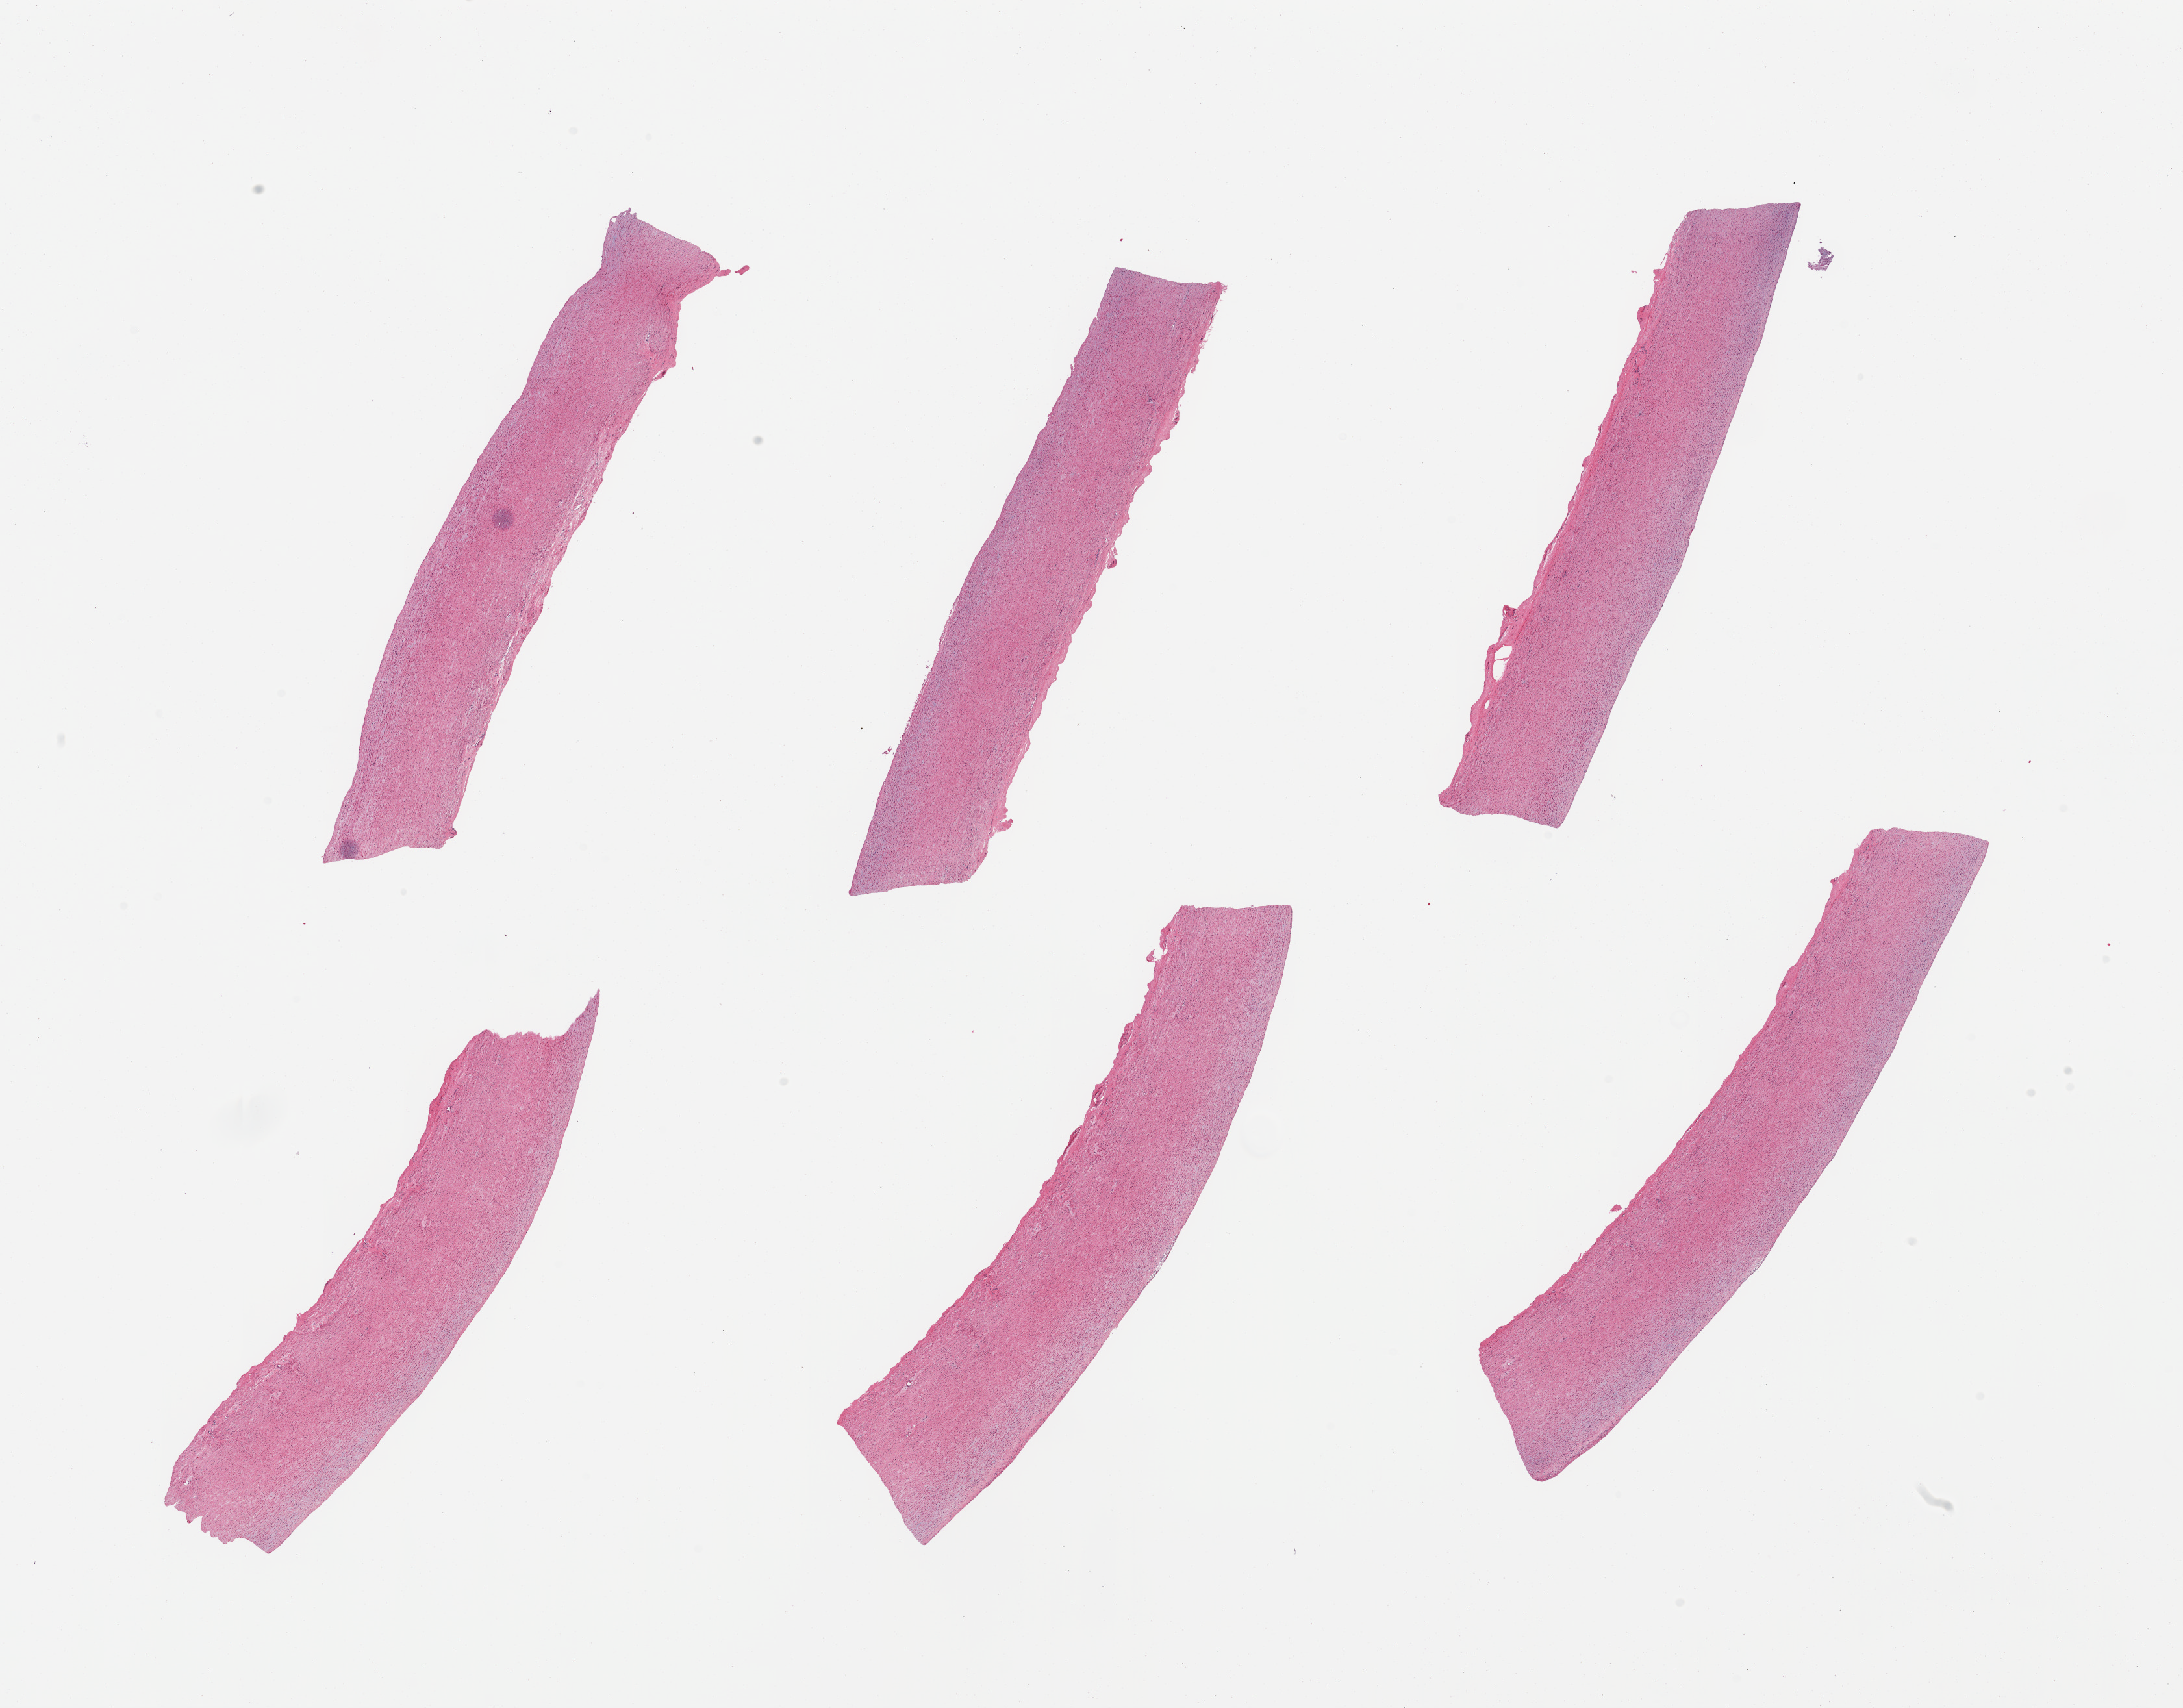
Whole-slide image, H&E stain, brightfield — a low-resolution overview of the entire scanned area, about 26.6 x 20.8 mm, PAXgene-fixed paraffin-embedded (PFPE) section, sampled site (target tissue): aorta, donor tissue sample. Donor: female.
Review note (as recorded): 6 pieces; focal mild atherosis.